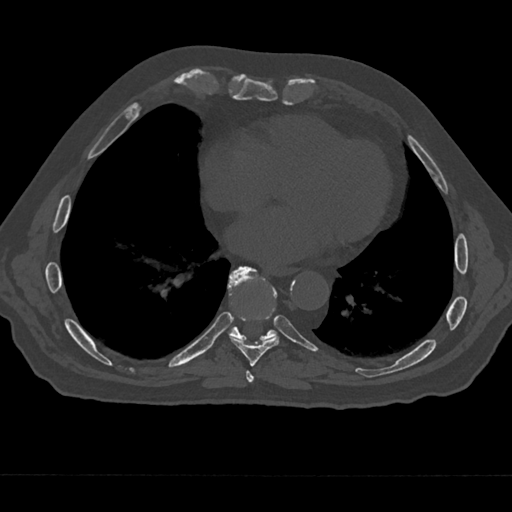
CT including the spine, one axial slice. Slice 296 of 797 in the series (ordered by position). Bone window (W 1800 / L 400 HU). 0.5 mm slice thickness. 512 × 512 image matrix. Male patient, age 75 years. Case-level facts recorded for this patient, not image findings: primary cancer: renal; vertebrae with lytic lesions (as recorded): T4.
Outlined on this slice (semi-automatically segmented with operator editing):
- T7 vertebra: bounding box (x1, y1, x2, y2) in pixels: (244, 370, 259, 385)
- T8 vertebra: (230, 268, 280, 366)
- T9 vertebra: (227, 266, 277, 341)